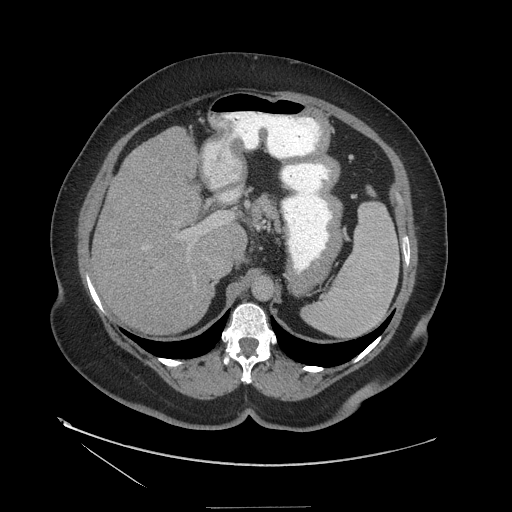
Contrast-enhanced abdominal CT (liver protocol), one axial slice. Reconstruction kernel STANDARD. 140 kVp. Soft-tissue window (W 400 / L 40 HU). 512 × 512 image matrix, field of view 480 × 480 mm. From the clinical record (not read from this slice): diagnosis: hepatocellular carcinoma (patient treated with transarterial chemoembolisation; whether this scan precedes or follows treatment is not stated here); TNM stage (as recorded): Stage-II; Child-Pugh class: A; tumour differentiation: well differentiated; tumour nodularity: multinodular.
Structures marked on this image (semi-automatic segmentation, software-assisted and operator-edited):
- liver parenchyma outside the tumour (the mass and vessels are separate outlines, so this box may not span the whole liver): box from (x=92, y=128) to (x=246, y=334) px
- liver vessels: (x=182, y=175)–(x=237, y=238)